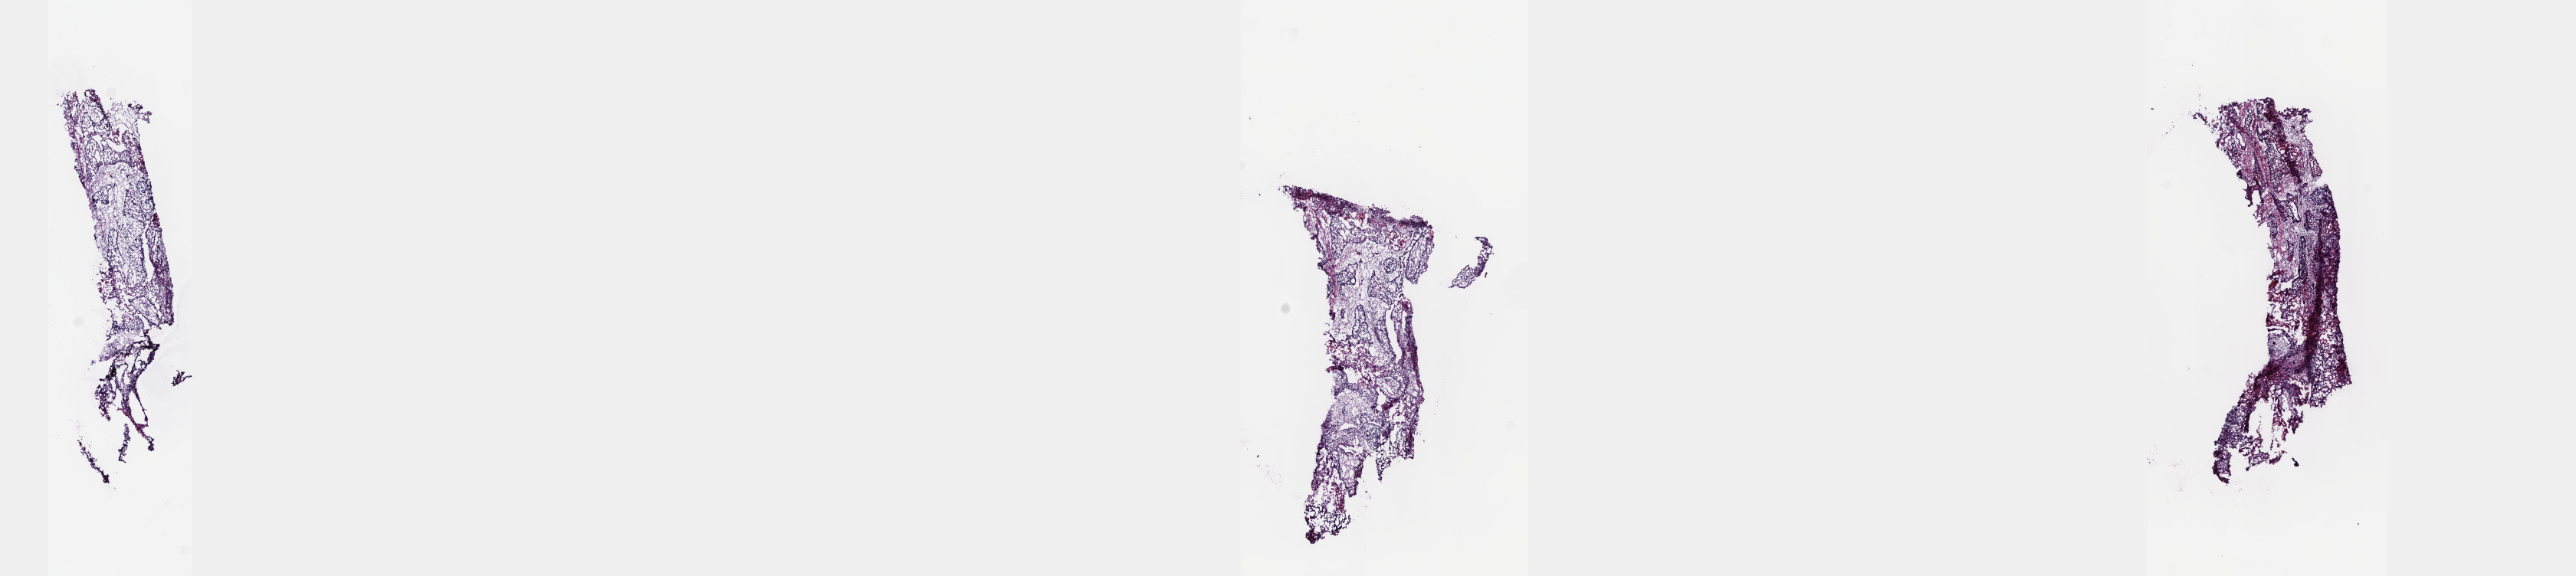
H&E-stained whole-slide image, whole scanned area (about 27.2 x 6.1 mm, acquisition: 40x scan) shown as a low-resolution overview. Frozen section from the top of the tissue portion. Sample: primary tumour, esophagus. Patient: male, age at initial diagnosis 57 years. Histologic grade: G2 (moderately differentiated). Slide review estimates, as recorded: tumour cells 25%, tumour nuclei 60%, normal cells 0%, stromal cells 60%, necrosis 15%. Infiltration values recorded for this section: lymphocyte infiltration 40%, monocyte infiltration 1%, neutrophil infiltration 1%.
AJCC pathologic stage: IIIB. Diagnosis: Squamous cell carcinoma, NOS (middle third of esophagus). Lymph nodes positive (case pathology): 4 of 13 examined.